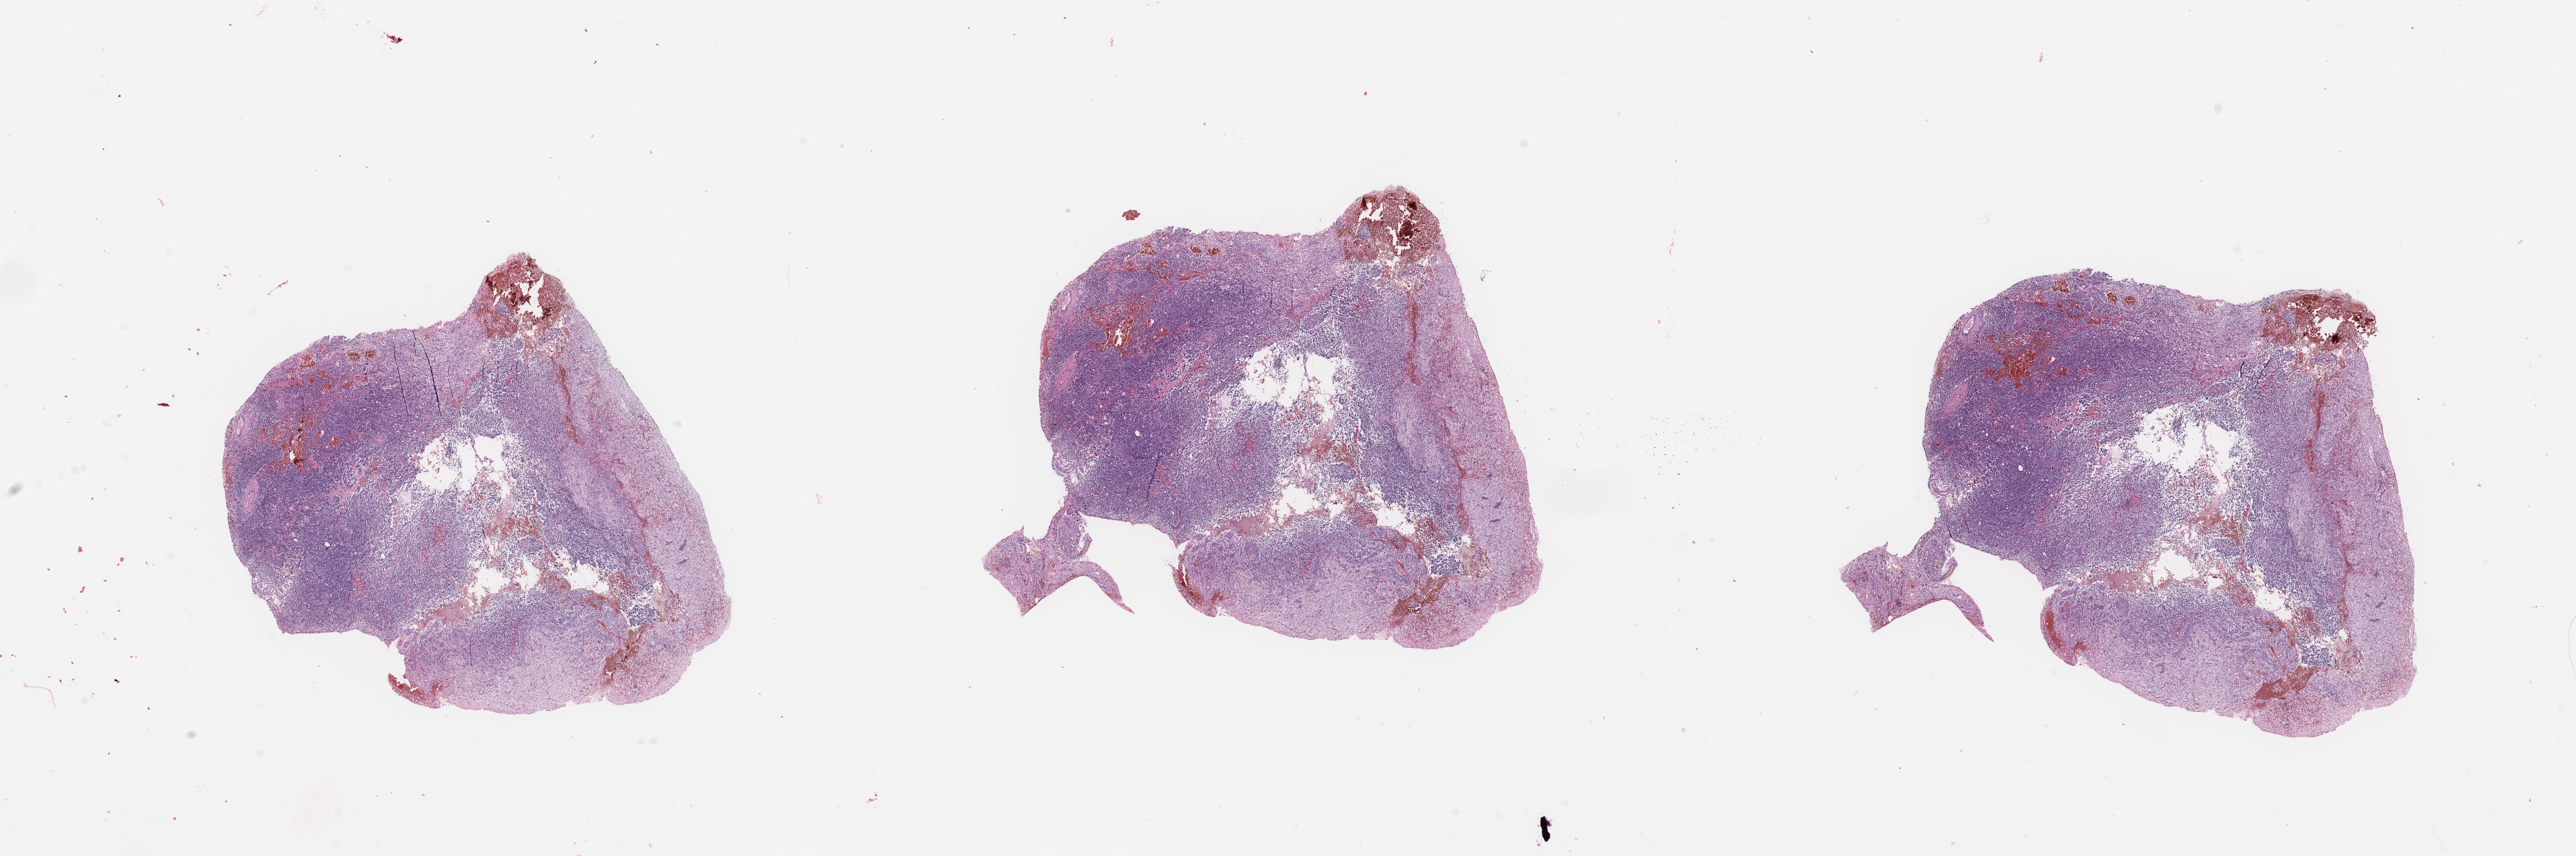
Whole-slide histology image, H&E, whole scanned area (about 30.5 x 10.1 mm) shown as a low-resolution overview. Tumour tissue sample, brain. Female, 60 y/o.
- primary tumour site (as recorded): parietal lobe
- diagnosis: Glioblastoma